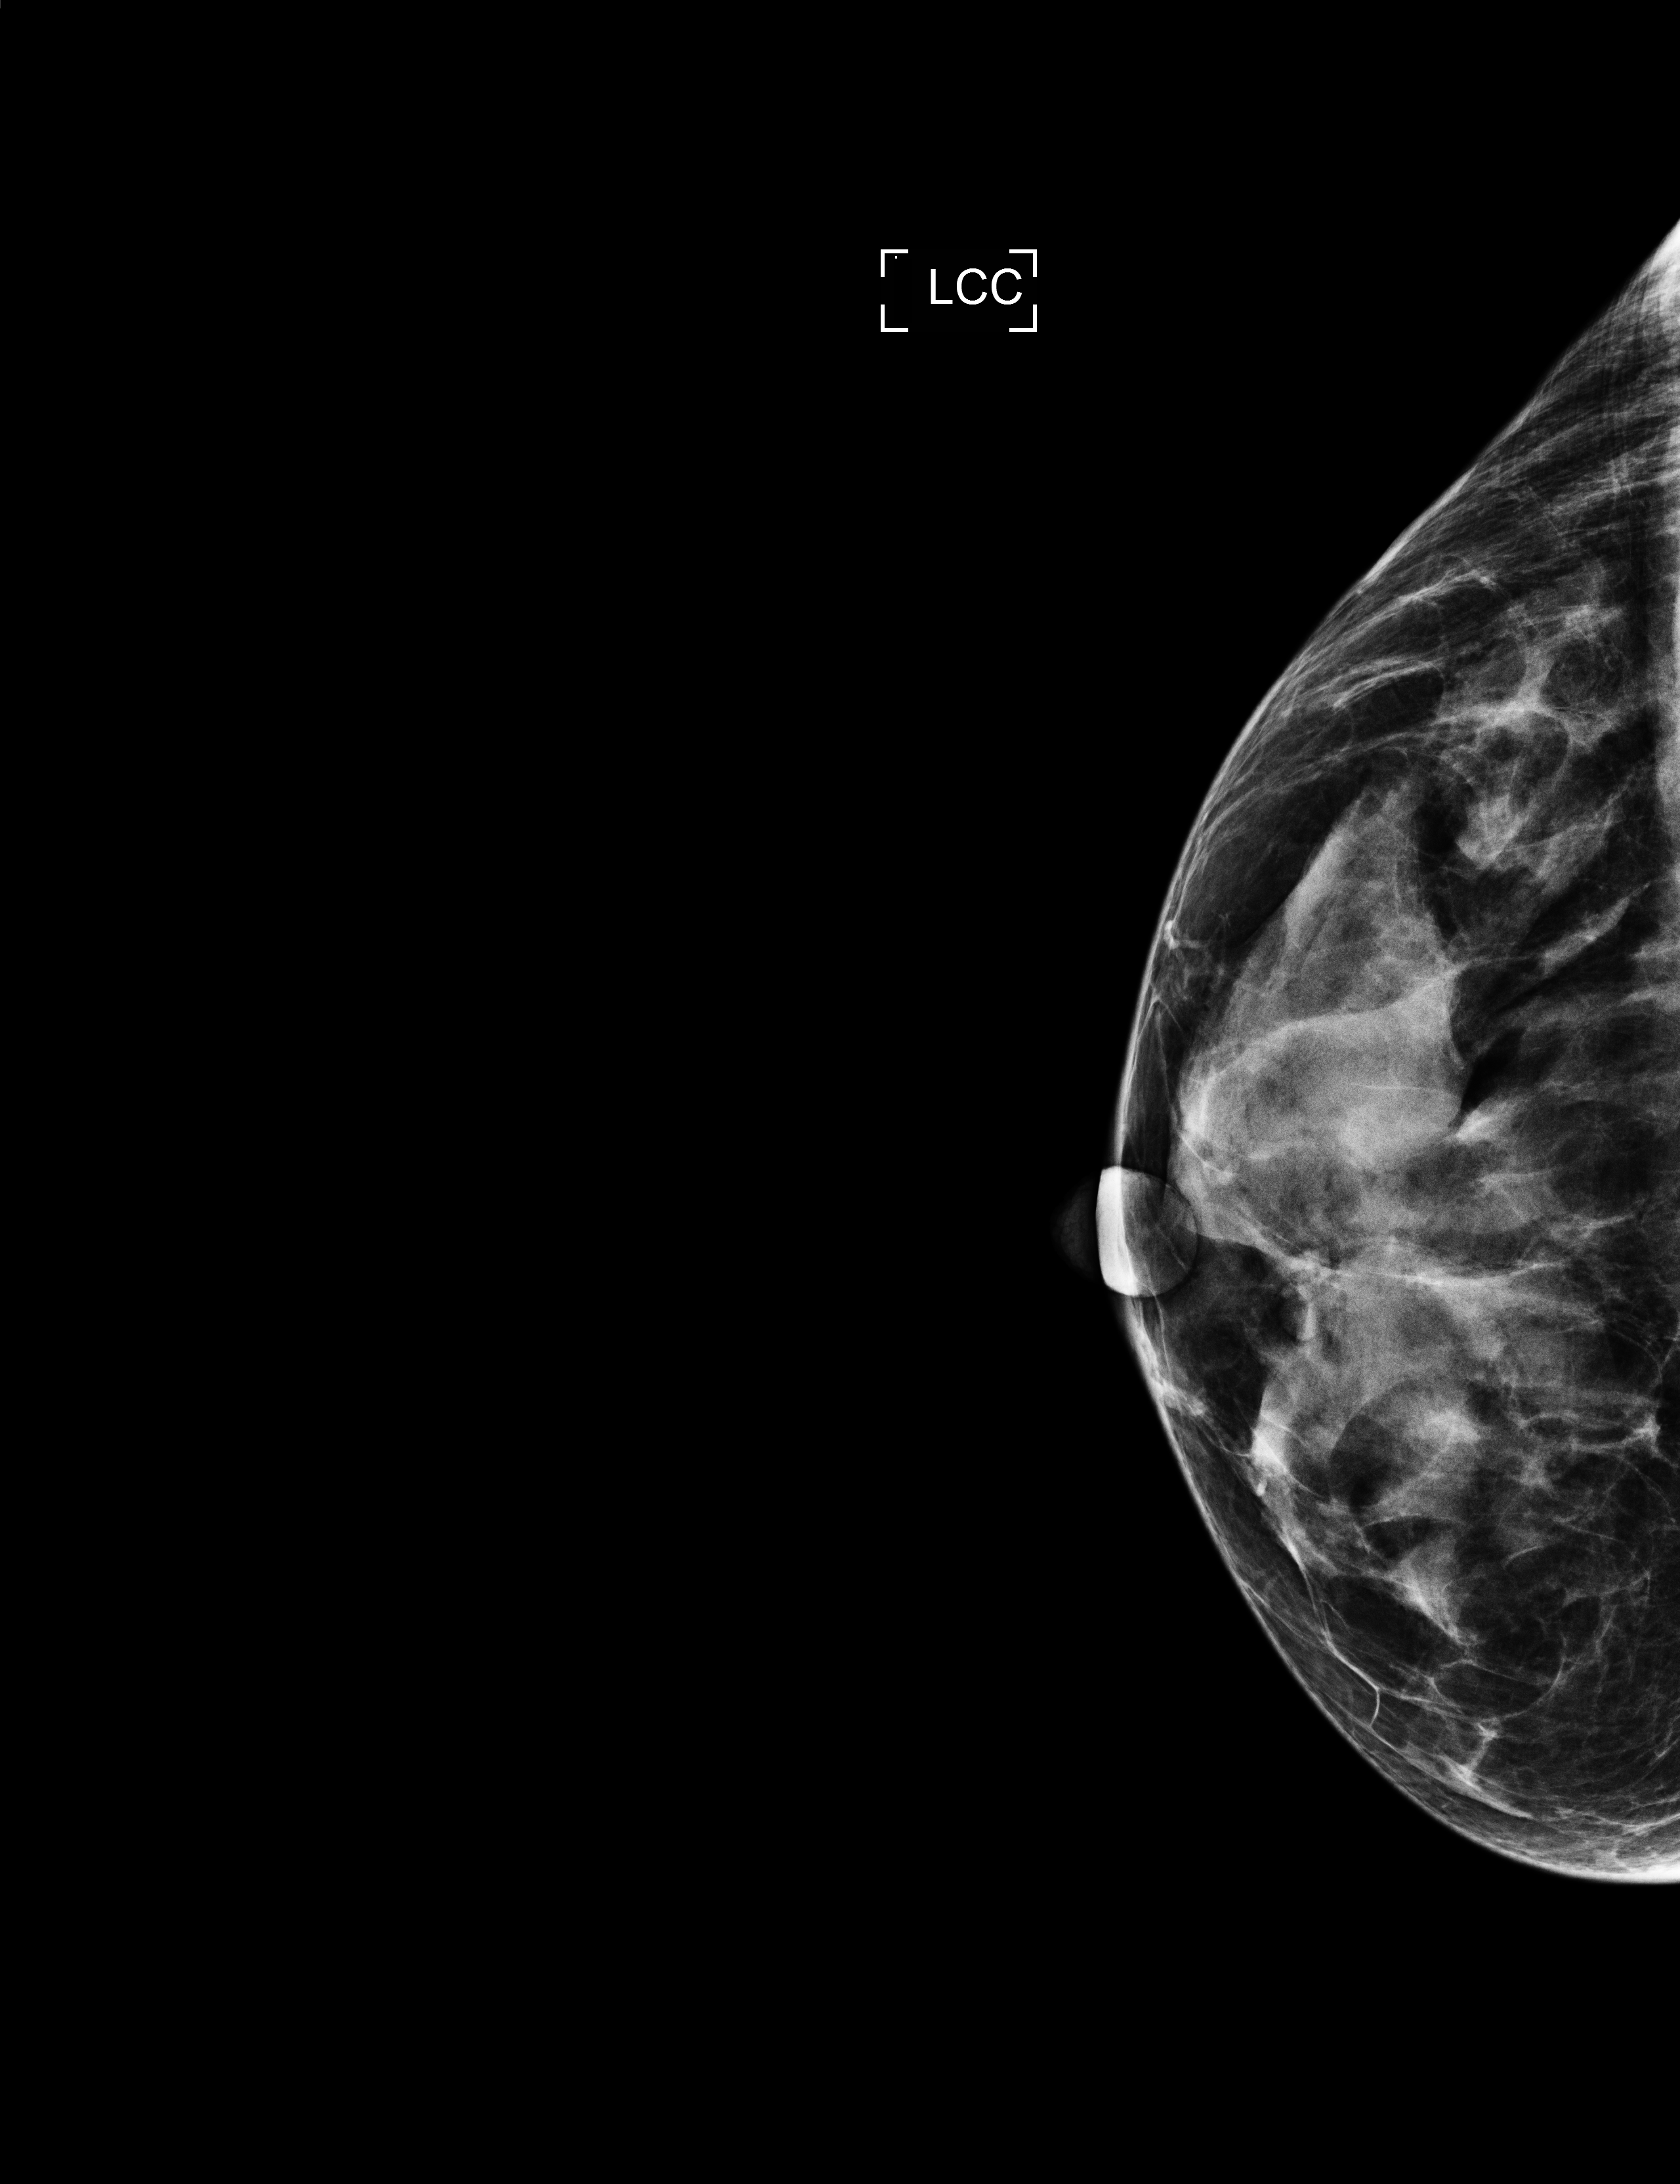
Screening examination. Female patient, age 54 years.
Image type: full-field digital mammogram. Breast: left. Projection: CC view.